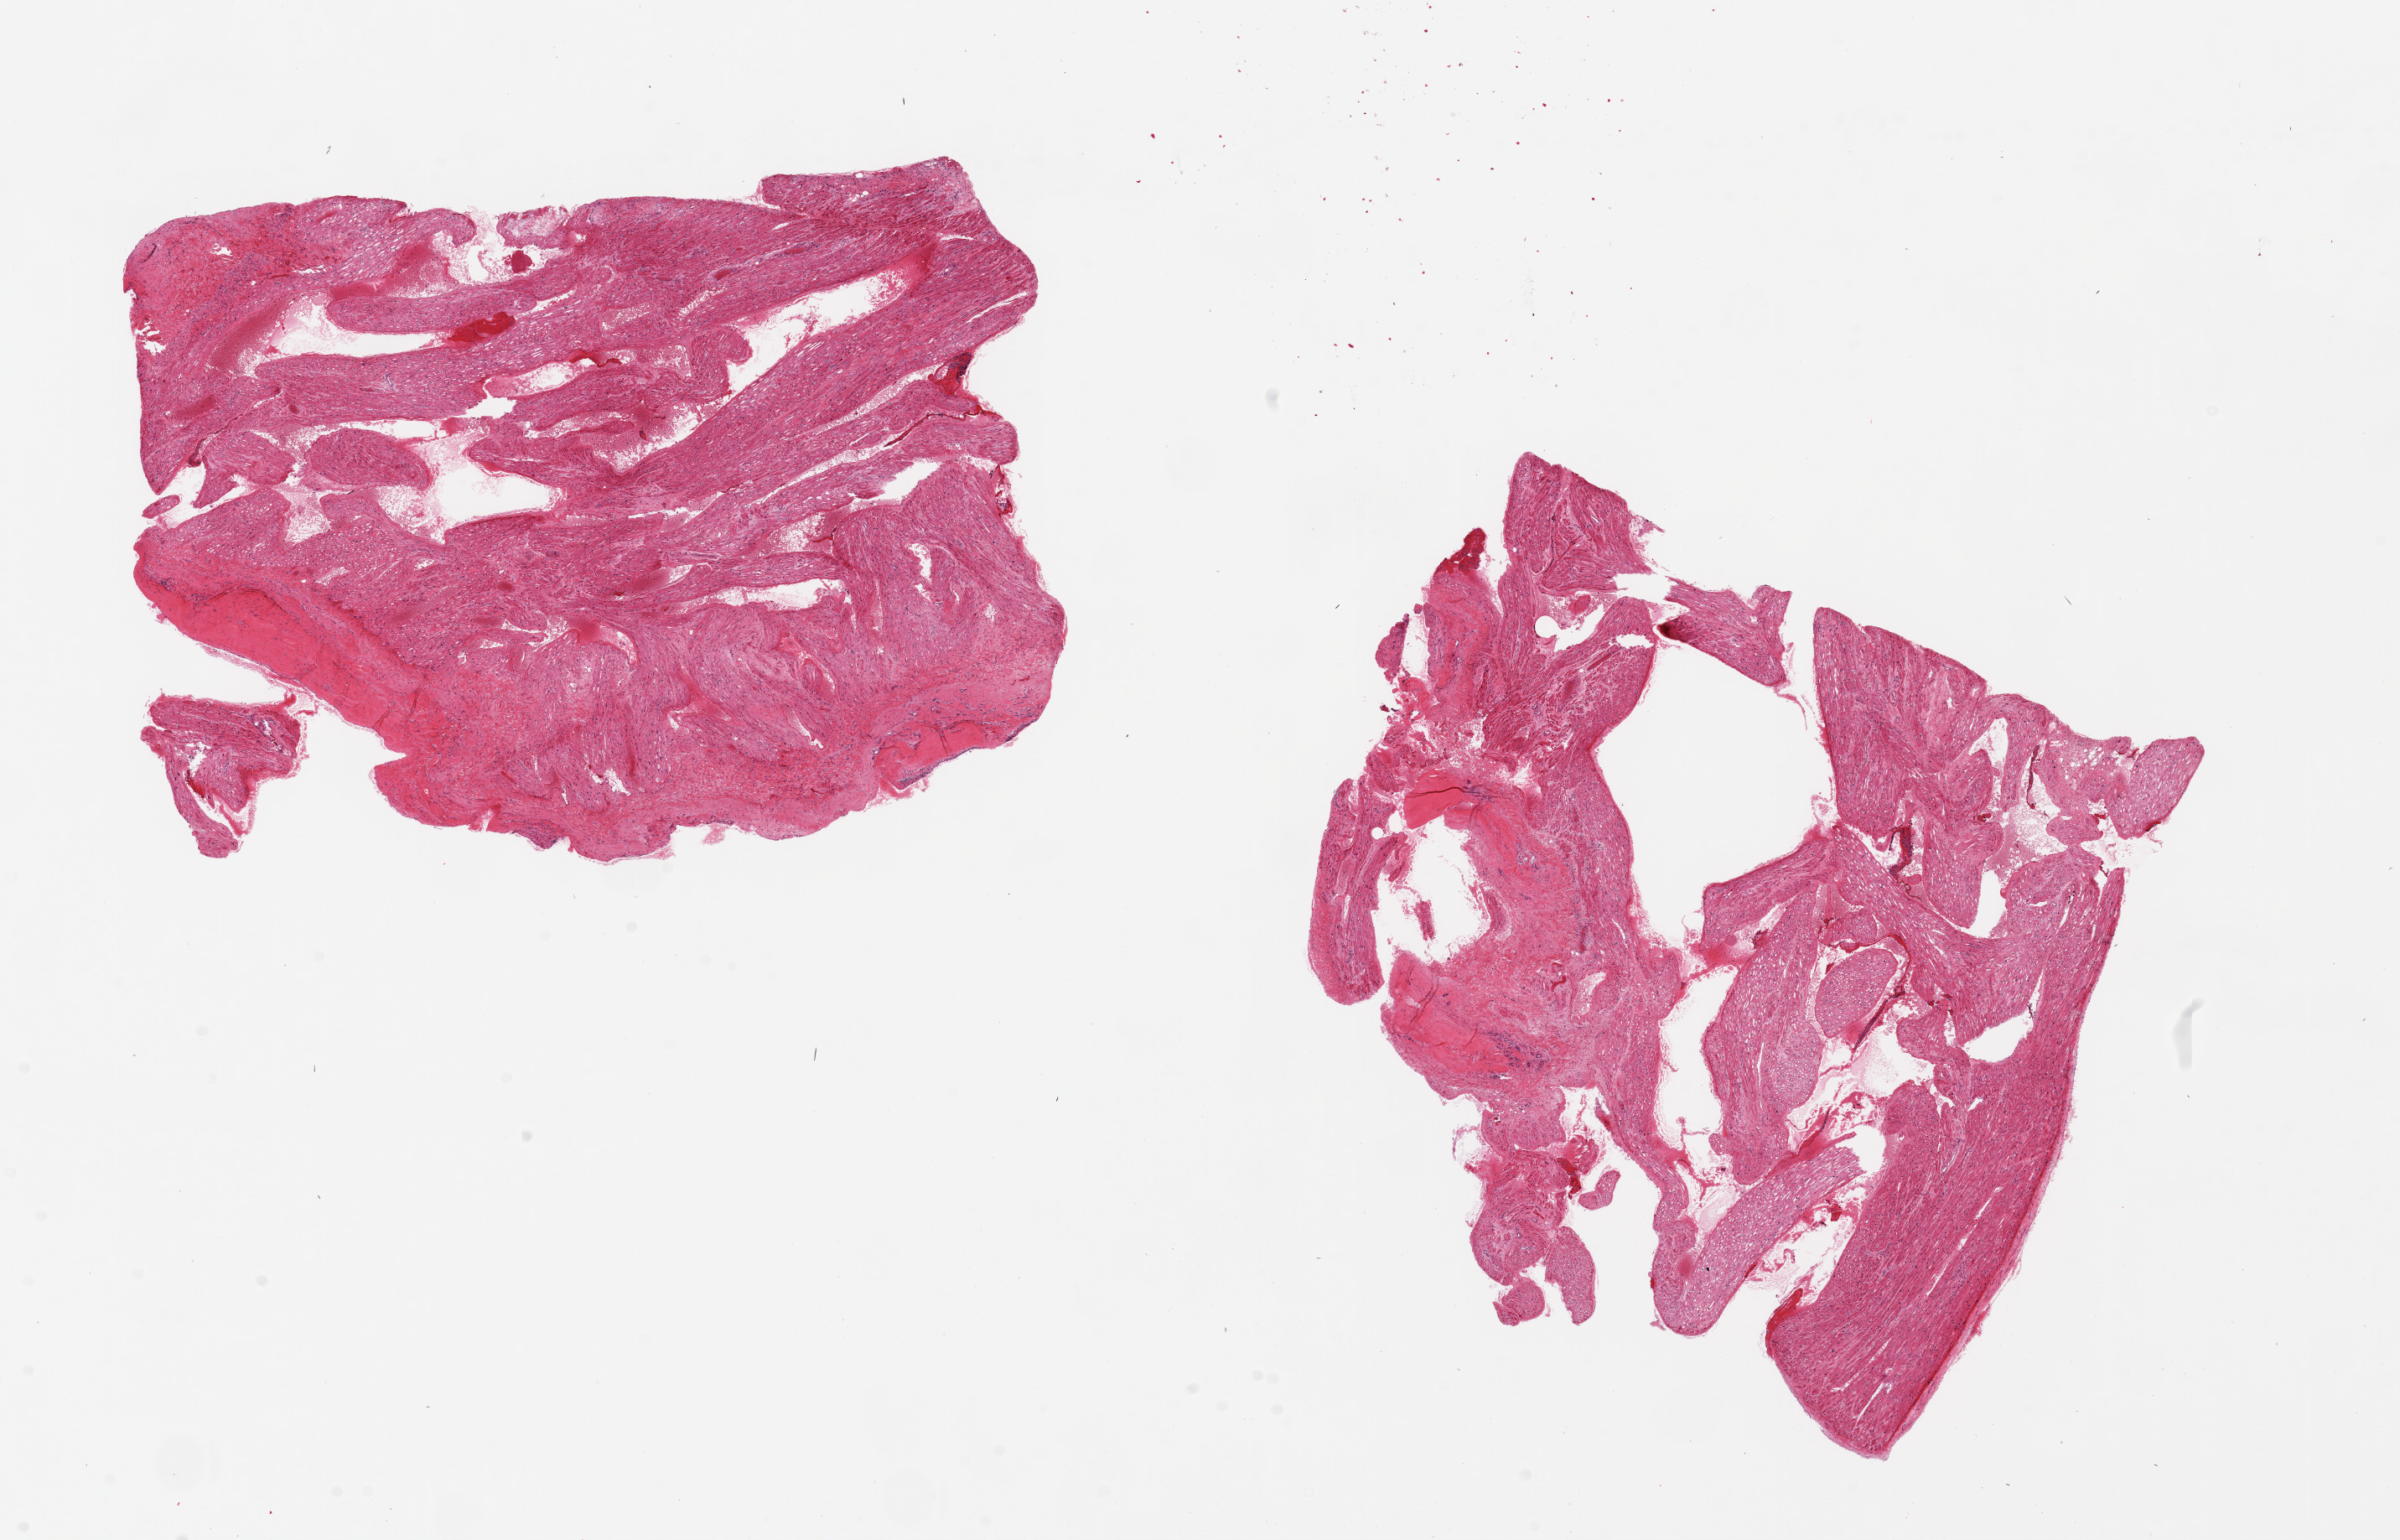
Digitized haematoxylin and eosin-stained section, whole scanned area (about 22.6 x 14.5 mm, slide scanned at 20x) shown as a low-resolution overview, PAXgene-fixed, paraffin-embedded tissue, sampled site (target tissue): auricular appendage, tissue donor sample. Male donor.
• pathologist's review note for this sample: 2 pieces, 9x6.5 & 8x7mm; no fat